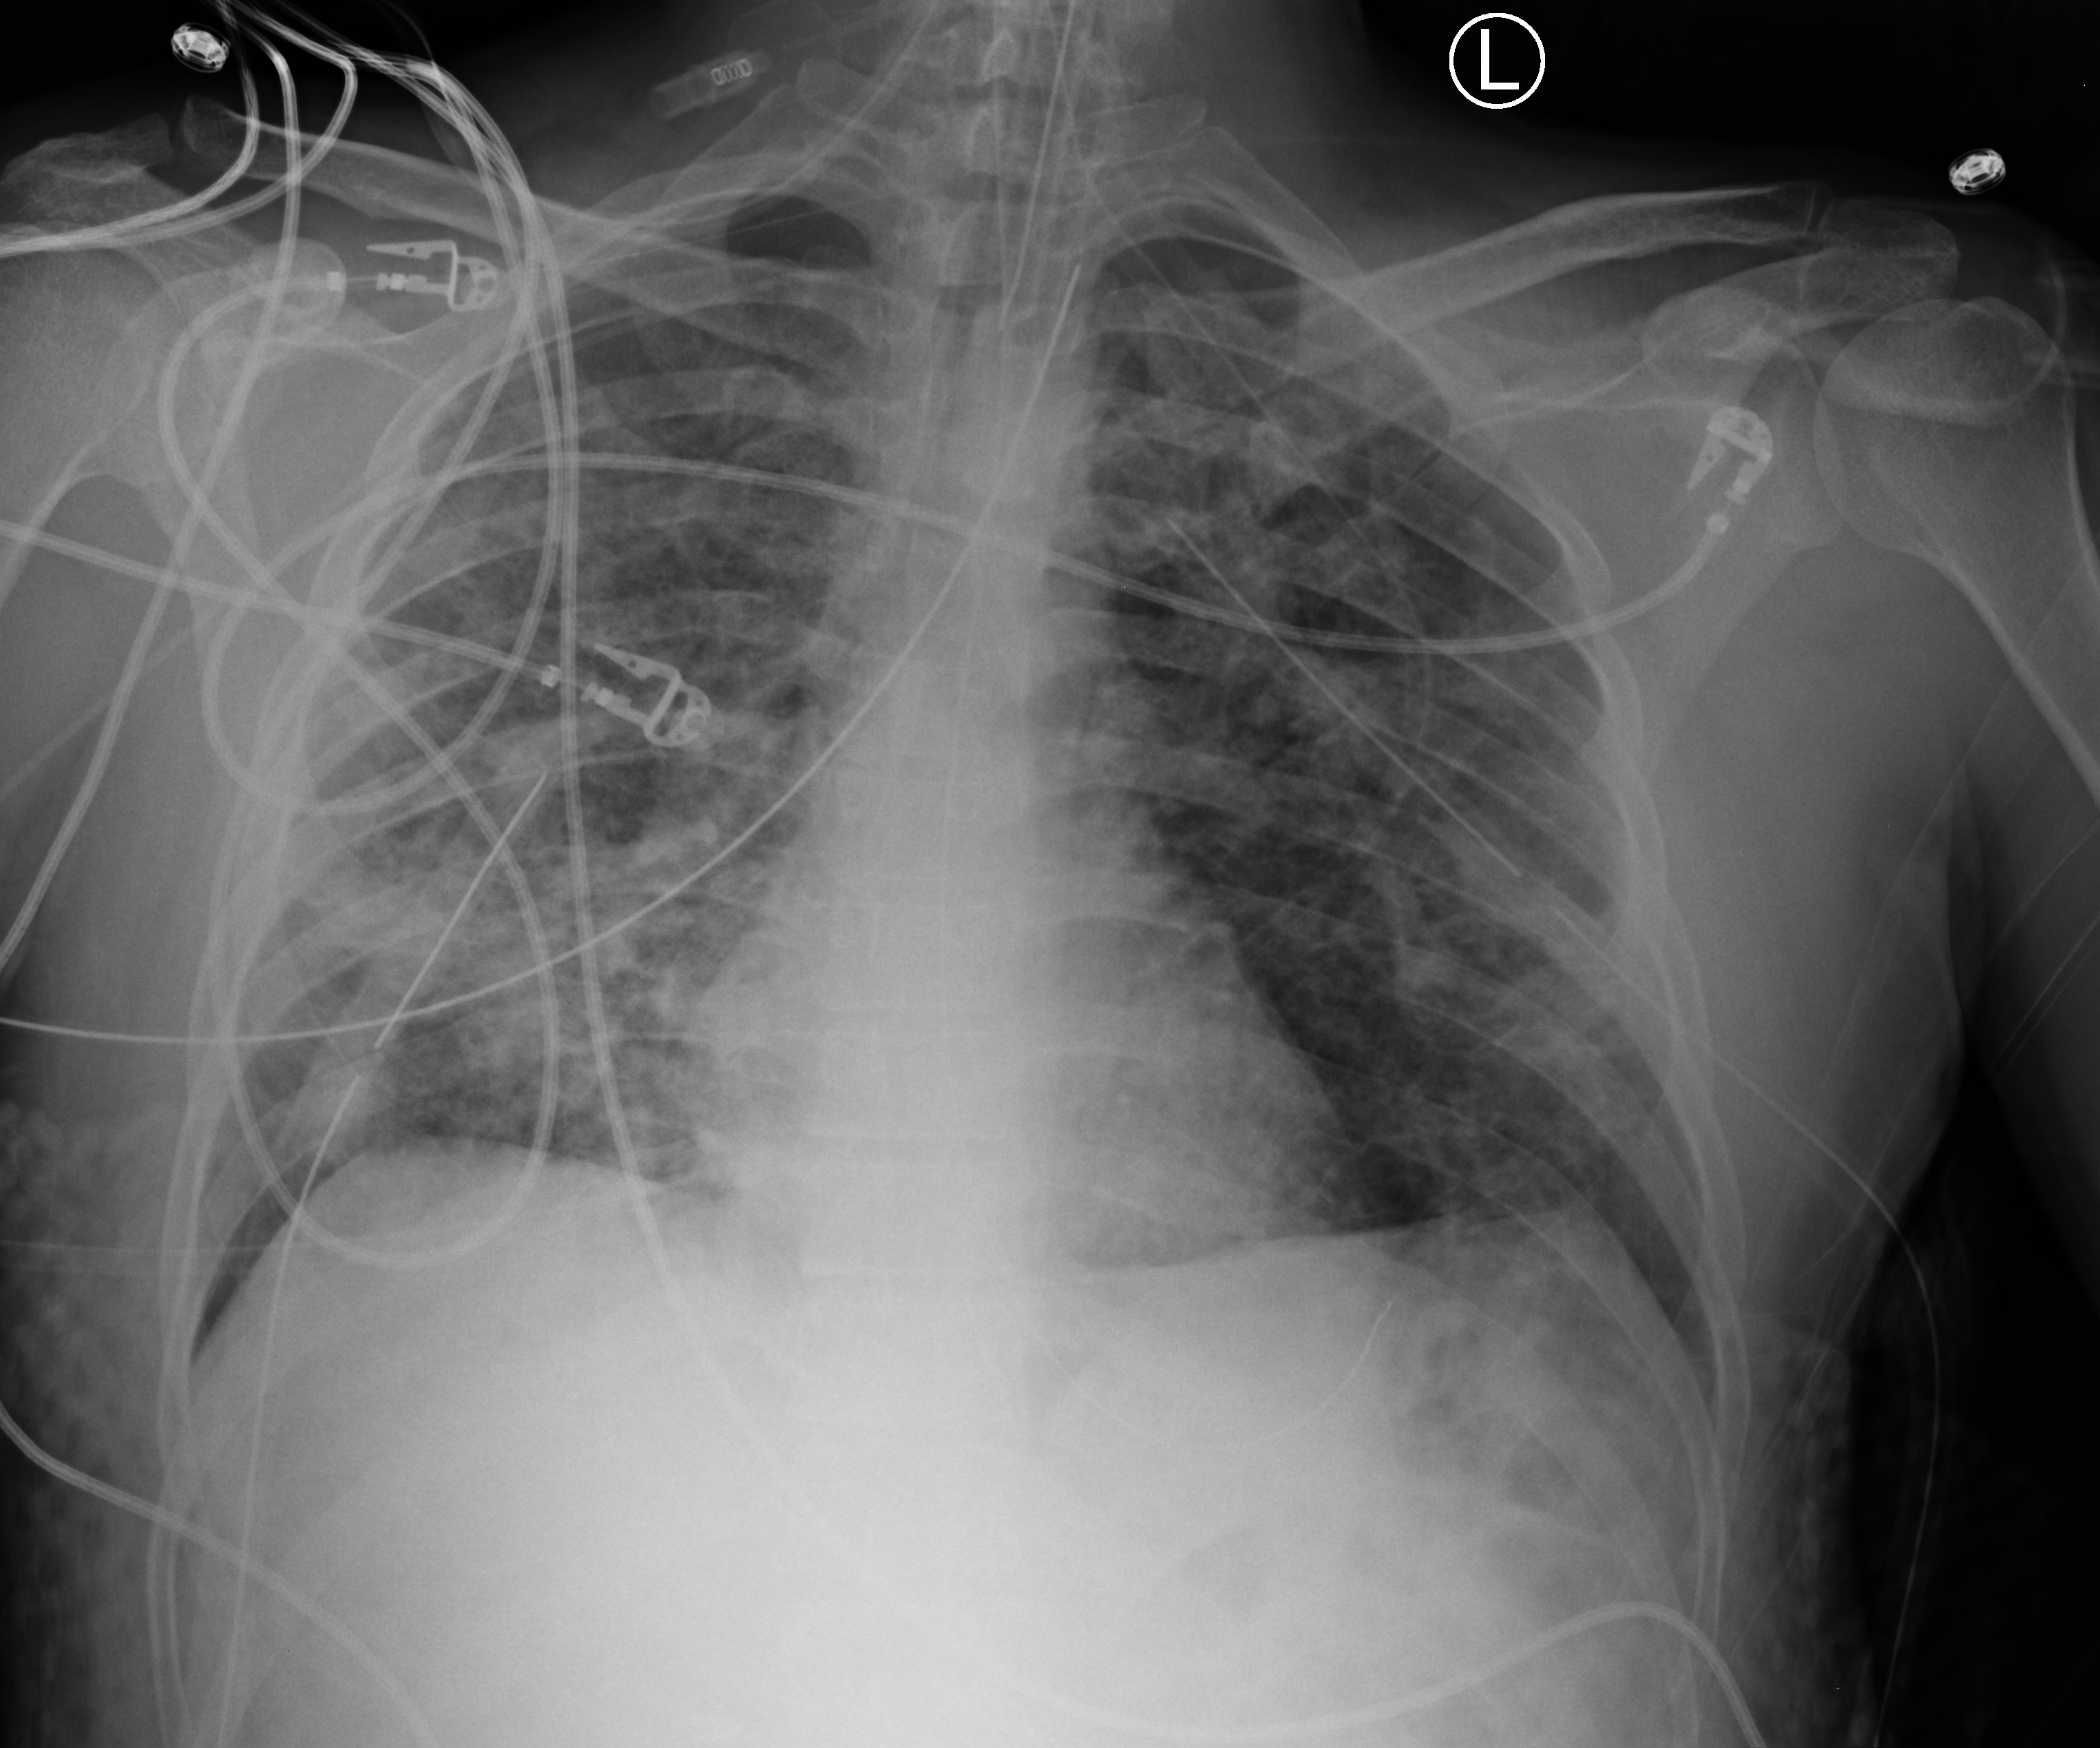
Chest X-ray (portable); anteroposterior (AP) projection. Patient hospitalised with COVID-19; male, aged 18–59 years.
Admission-level facts for this patient (not findings on this image; timing relative to this image not recorded): length of hospital stay: 29 days.